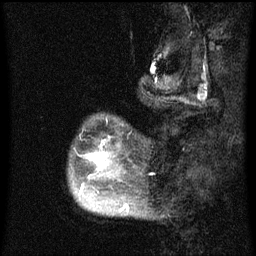
Breast MRI (dynamic contrast-enhanced), one sagittal slice. Position 12 of 60 along the scan axis. Dynamic contrast-enhanced series, image 2 of 3 at this slice position (ordered by acquisition). 1.5 T. TE 4.2 ms, TR 8 ms. 2 mm slice thickness. 256 × 256 image matrix, field of view 190 × 190 mm. Patient: female, 50 years.
Outlined on this slice (semi-automatically segmented with operator editing):
- analysis volume of interest (the breast-tissue region the enhancement analysis was run in; not a lesion): bounding box (x1, y1, x2, y2) in pixels: (69, 118, 142, 216)
- tumour enhancement mask (voxels above the 70 % enhancement threshold inside the analysis volume of interest): (79, 150, 129, 212)